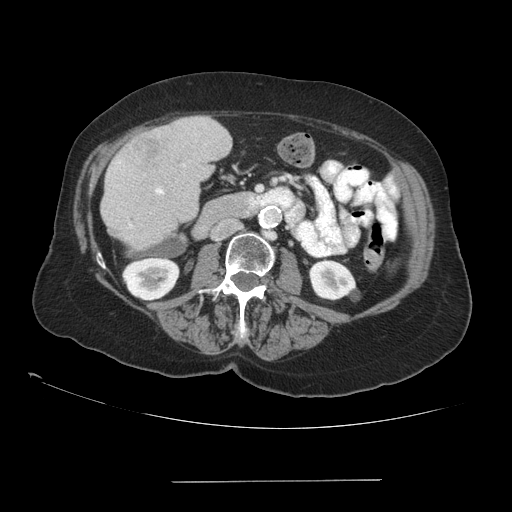
Contrast-enhanced abdominal CT (liver protocol), one axial slice; position 29 of 89 along the scan axis; soft-tissue window (W 400 / L 40 HU); 2.5 mm slice thickness; 512 × 512 image matrix, field of view 400 × 400 mm. Case-level facts recorded for this patient, not image findings: diagnosis: hepatocellular carcinoma (patient treated with transarterial chemoembolisation; whether this scan precedes or follows treatment is not stated here); TNM stage (as recorded): Stage-IVA; Child-Pugh class: A; tumour differentiation: poorly differentiated; tumour nodularity: uninodular.
Outlined on this slice (semi-automatic segmentation, software-assisted and operator-edited):
- liver parenchyma outside the tumour (the mass and vessels are separate outlines, so this box may not span the whole liver): bounding box [x1, y1, x2, y2] px = [100, 116, 232, 250]
- mass: [128, 130, 162, 162]
- liver vessels: [130, 188, 164, 227]